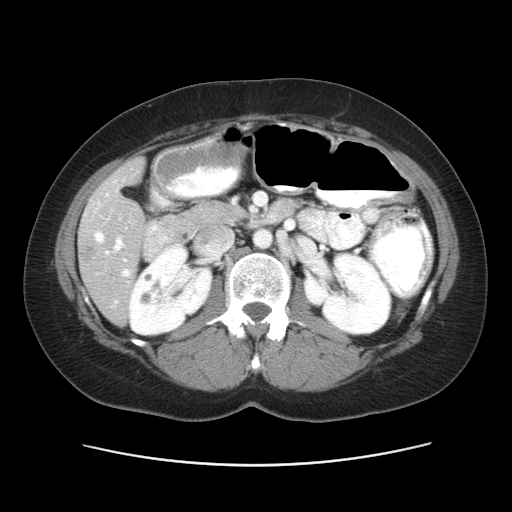
Contrast-enhanced abdominal CT, one axial slice. Slice 24 of 52 in the series (ordered by position). Reconstruction kernel STANDARD. 120 kVp. Intravenous contrast given. Soft-tissue window (W 400 / L 40 HU). 5 mm slice thickness. 512 × 512 image matrix. Female patient, age 48 years. From the clinical record (not read from this slice): diagnosis: colorectal cancer liver metastases, imaged before liver resection; multiple liver metastases: yes; largest metastasis: 4.5 cm; chemotherapy before resection: yes.
Annotated regions visible in this slice (outlined manually by an expert reader):
- hepatic veins: bounding box [x1, y1, x2, y2] px = [95, 232, 130, 276]
- liver: [79, 159, 145, 324]
- portal vein (with intrahepatic branches): [114, 237, 124, 251]
- liver metastasis: [80, 246, 97, 264]